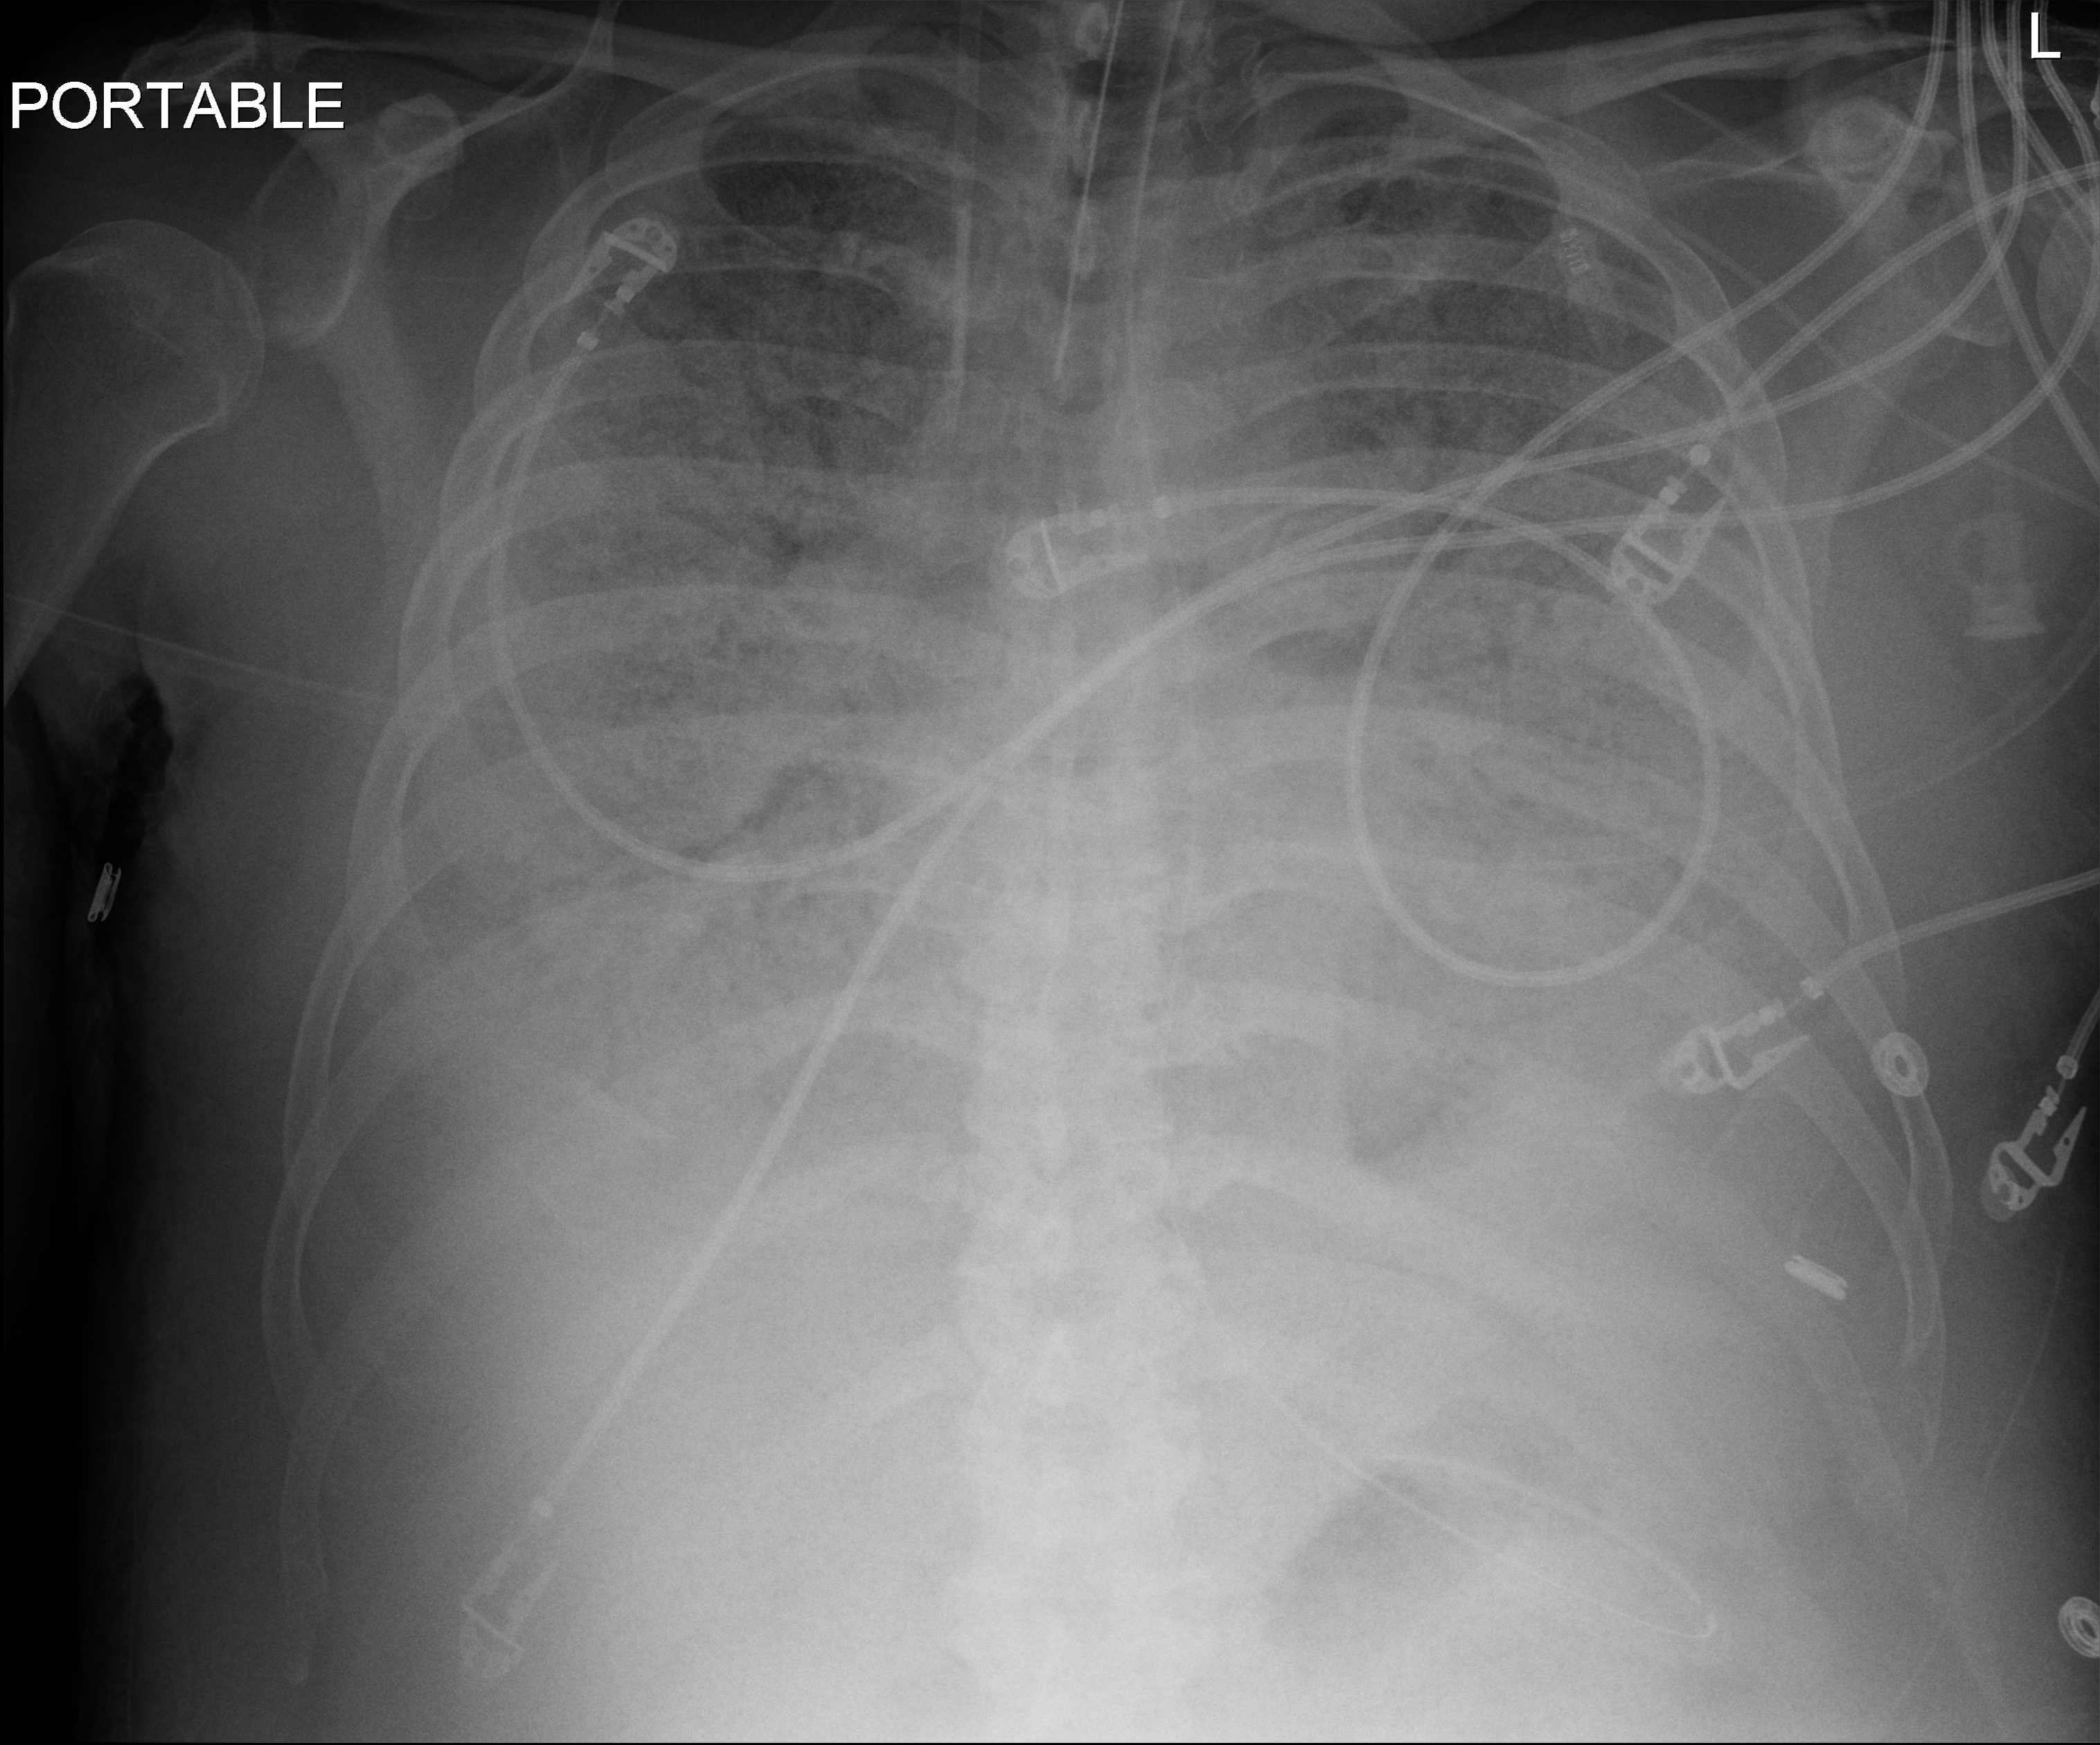
Bedside chest radiograph (digital radiography); anteroposterior (AP) projection. Male patient hospitalised with COVID-19, age 60–74 years.
From the hospital-stay record, not from the radiograph (when in the stay this image was taken is not recorded):
- mechanically ventilated during this hospital stay: yes
- chronic kidney disease (admission record): no